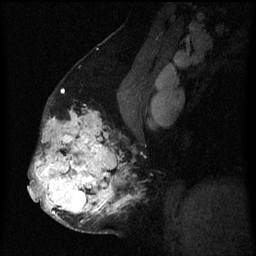
Breast MRI (dynamic contrast-enhanced), one sagittal slice; position 34 of 60 along the scan axis; dynamic contrast-enhanced series, image 2 of 3 at this slice position (ordered by acquisition); 1.5 T; TE 4.2 ms, TR 8 ms; 256 × 256 image matrix, field of view 190 × 190 mm. Patient: female, 50 years.
Structures marked on this image (semi-automatic segmentation, software-assisted and operator-edited):
- analysis volume of interest (the breast-tissue region the enhancement analysis was run in; not a lesion): box from (x=32, y=105) to (x=137, y=233) px
- tumour enhancement mask (voxels above the 70 % enhancement threshold inside the analysis volume of interest): (x=32, y=111)–(x=131, y=222)